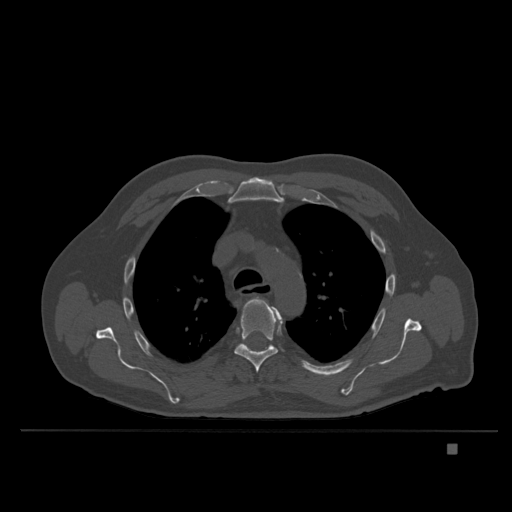
CT including the spine, one axial slice. Slice 274 of 435 in the series (ordered by position). Bone window (W 1800 / L 400 HU). 1.5 mm slice thickness. 512 × 512 image matrix, field of view 434 × 434 mm. Patient: male, 73 years. Case-level facts recorded for this patient, not image findings: primary cancer: skin.
Outlined on this slice (semi-automatic segmentation, software-assisted and operator-edited):
- T3 vertebra: bounding box [x1, y1, x2, y2] px = [269, 346, 271, 348]
- T4 vertebra: [257, 298, 262, 300]
- T5 vertebra: [234, 297, 283, 373]